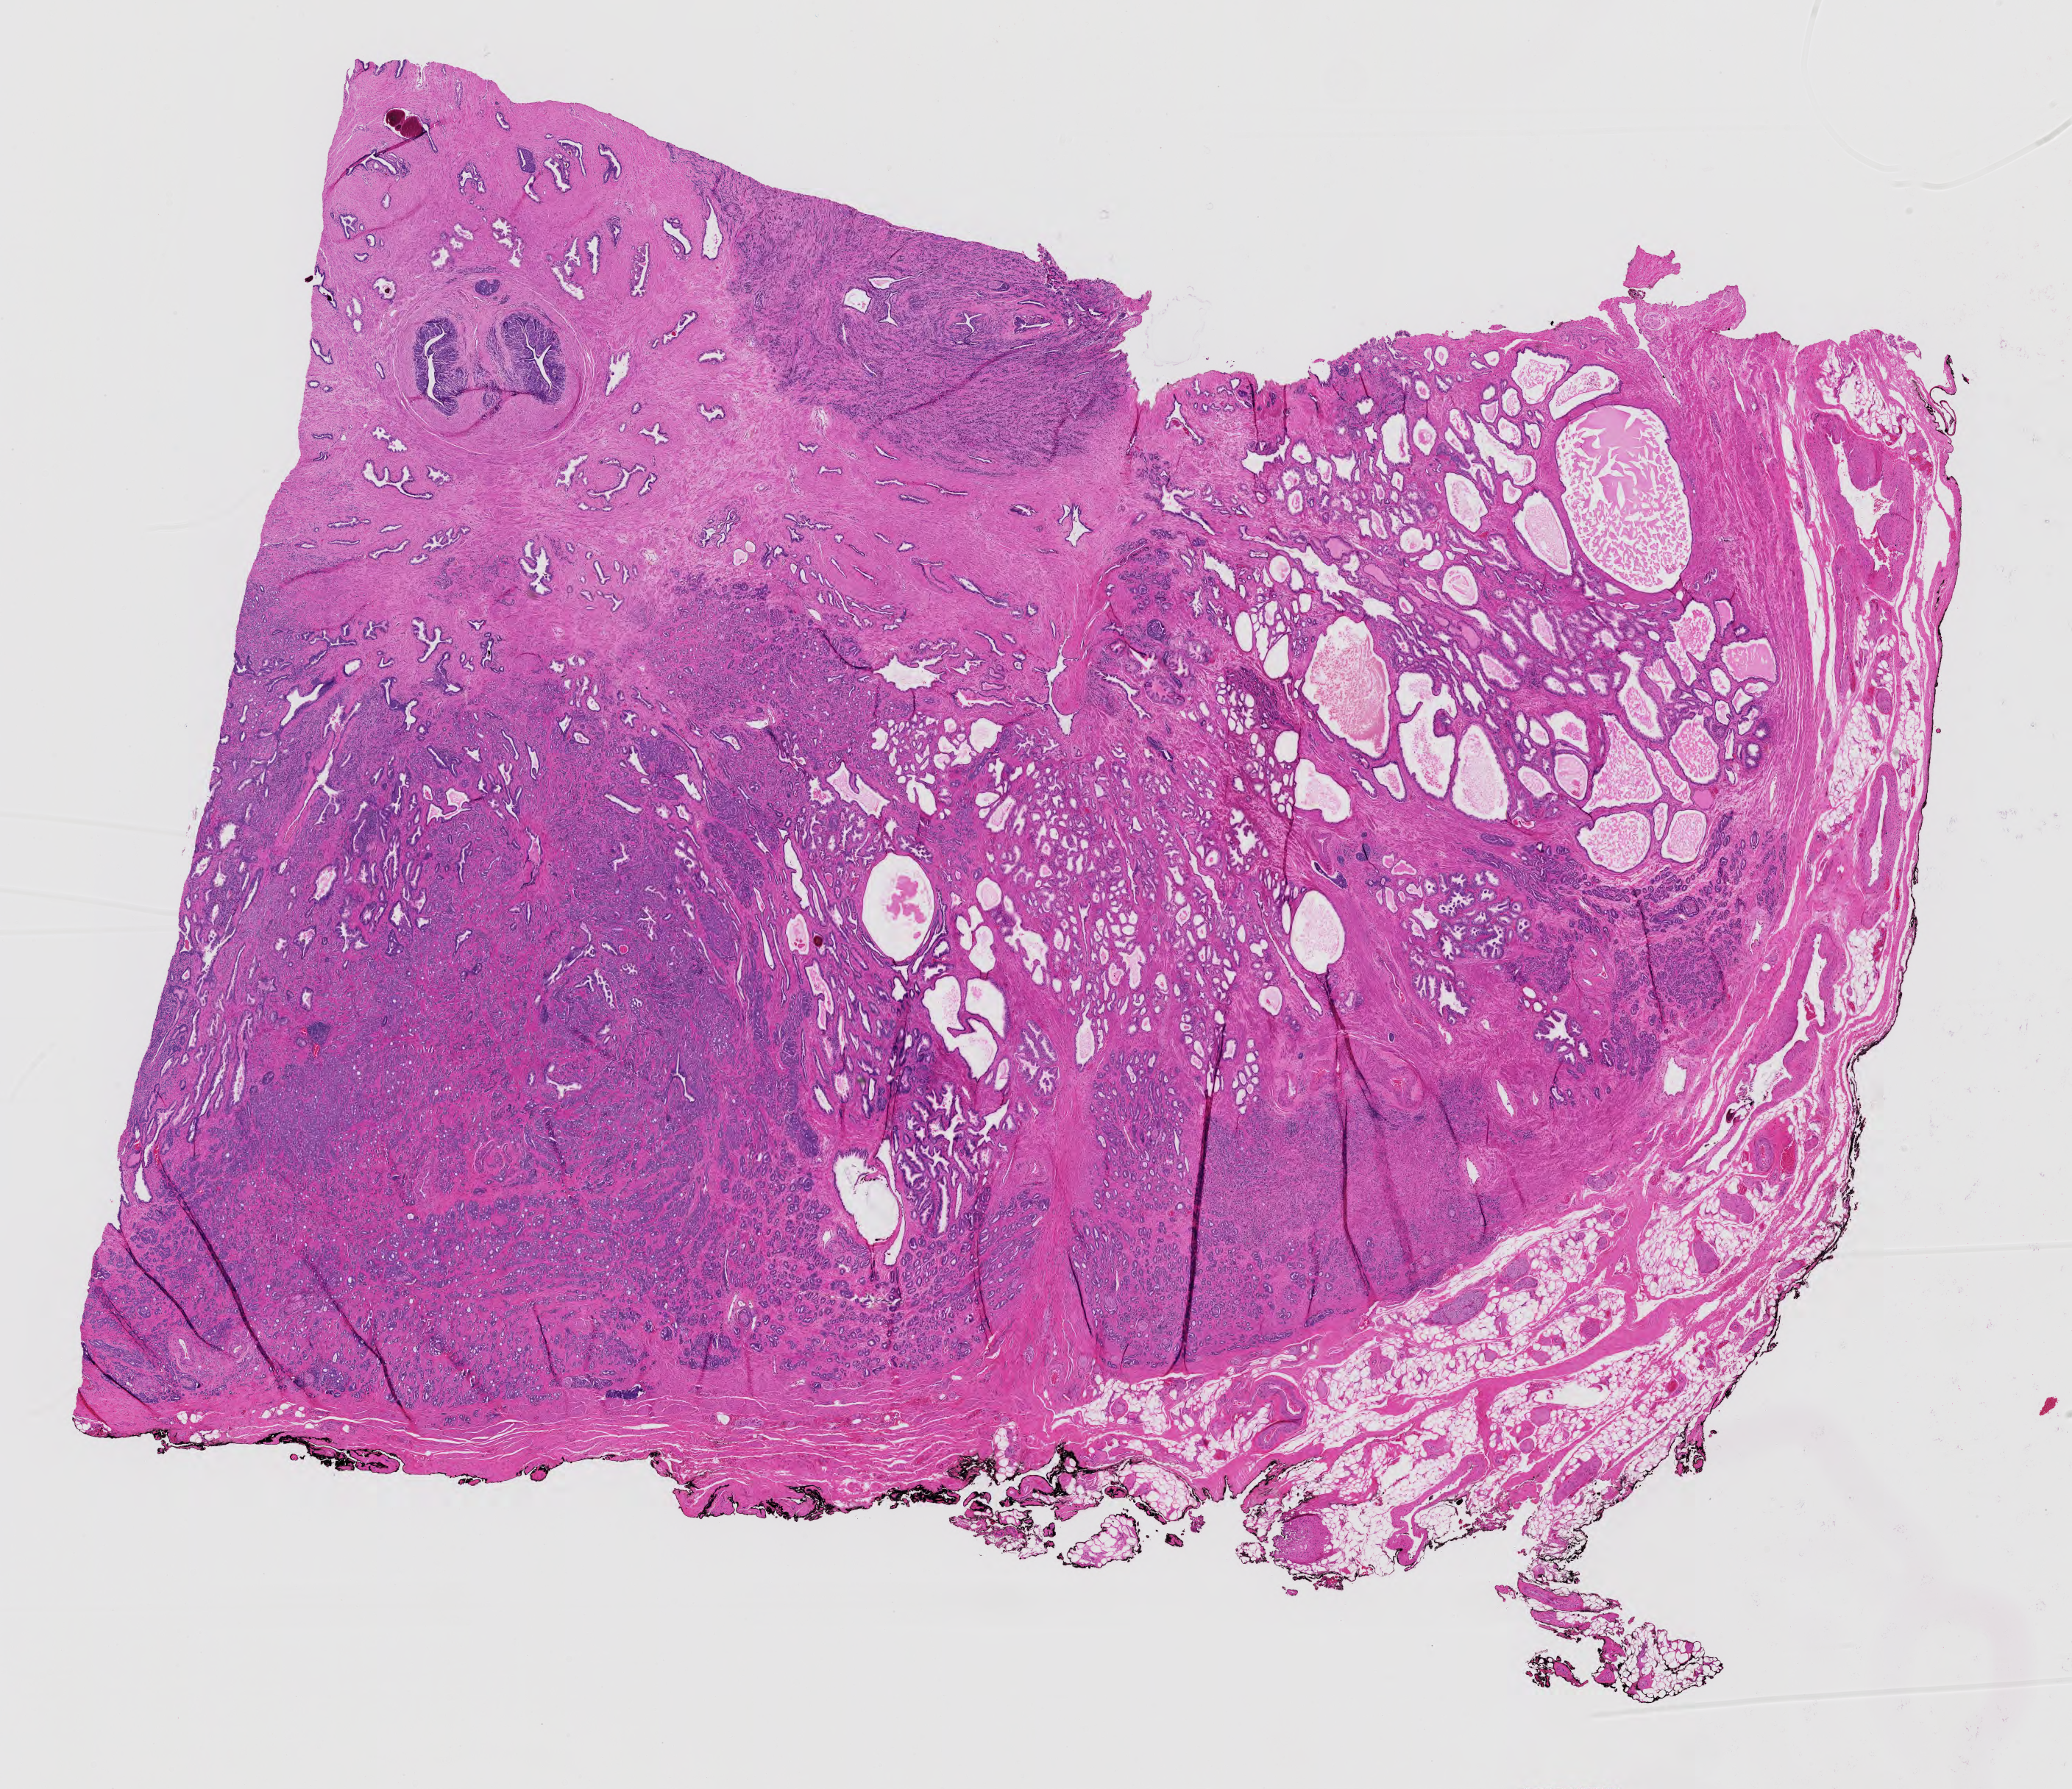
Whole-slide histology image, Hematoxylin and eosin (H&E) stained, whole scanned area (about 20.4 x 17.6 mm, acquisition: 40x scan) shown as a low-resolution overview. Formalin-fixed paraffin-embedded (FFPE) diagnostic section. Sample: primary tumour, prostate. Patient: male, age at initial diagnosis 67 years. Gleason score: 9 (4+5).
• lymph nodes positive (case pathology): 4 of 20 examined
• laterality: bilateral
• histologic diagnosis: Adenocarcinoma, NOS (prostate gland)